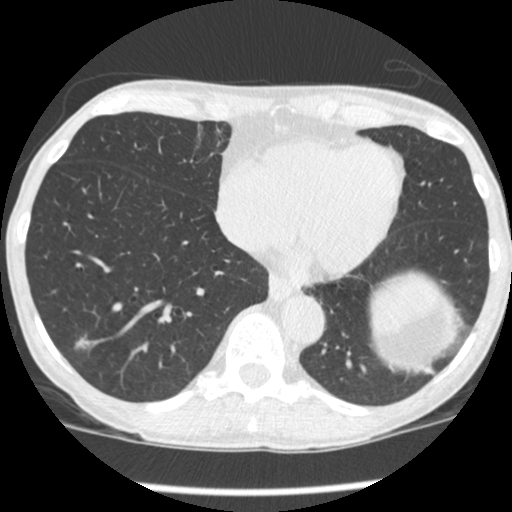
Low-dose screening chest CT, one axial slice. Position 84 of 248 along the scan axis. Reconstruction kernel STANDARD. 120 kVp. Lung window (W 1500 / L -600 HU). 1.25 mm slice thickness. 512 × 512 image matrix, field of view 293 × 293 mm.
Annotated regions visible in this slice (manually delineated by an expert):
- lesion 1 (tumor, lower lobe of right lung): bounding box [x1, y1, x2, y2] px = [75, 335, 94, 349]